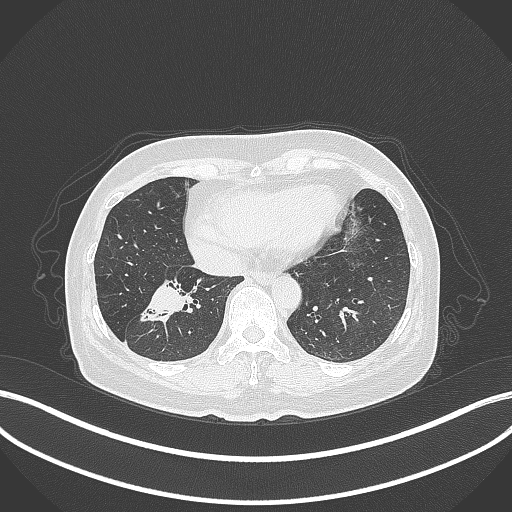
Chest CT, one axial slice. Position 120 of 429 along the scan axis. 120 kVp. Lung window (W 1500 / L -600 HU). 1 mm slice thickness. 512 × 512 image matrix, field of view 400 × 400 mm. Female patient, age 67 years. Case-level facts recorded for this patient, not image findings: clinical TNM (as recorded): T1c N1 M0; histopathological grade: G2-3.
Outlined on this slice (rectangle marked by the reading radiologist):
- lung tumour (recorded histology: adenocarcinoma): bounding box (x1, y1, x2, y2) in pixels: (135, 280, 194, 330)